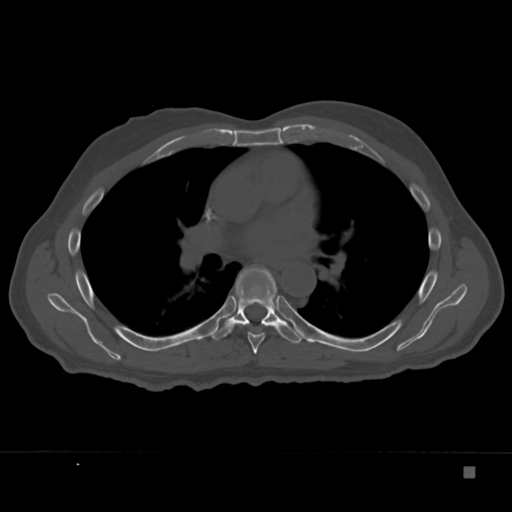
CT including the spine, one axial slice; position 231 of 332 along the scan axis; 120 kVp; bone window (W 1800 / L 400 HU); 512 × 512 image matrix, field of view 389 × 389 mm. Male patient, age 72 years. From the clinical record (not read from this slice): primary cancer: skeletal.
Structures marked on this image (semi-automatically segmented with operator editing):
- T6 vertebra: bounding box [x1, y1, x2, y2] px = [240, 274, 279, 354]
- T7 vertebra: [211, 266, 304, 344]